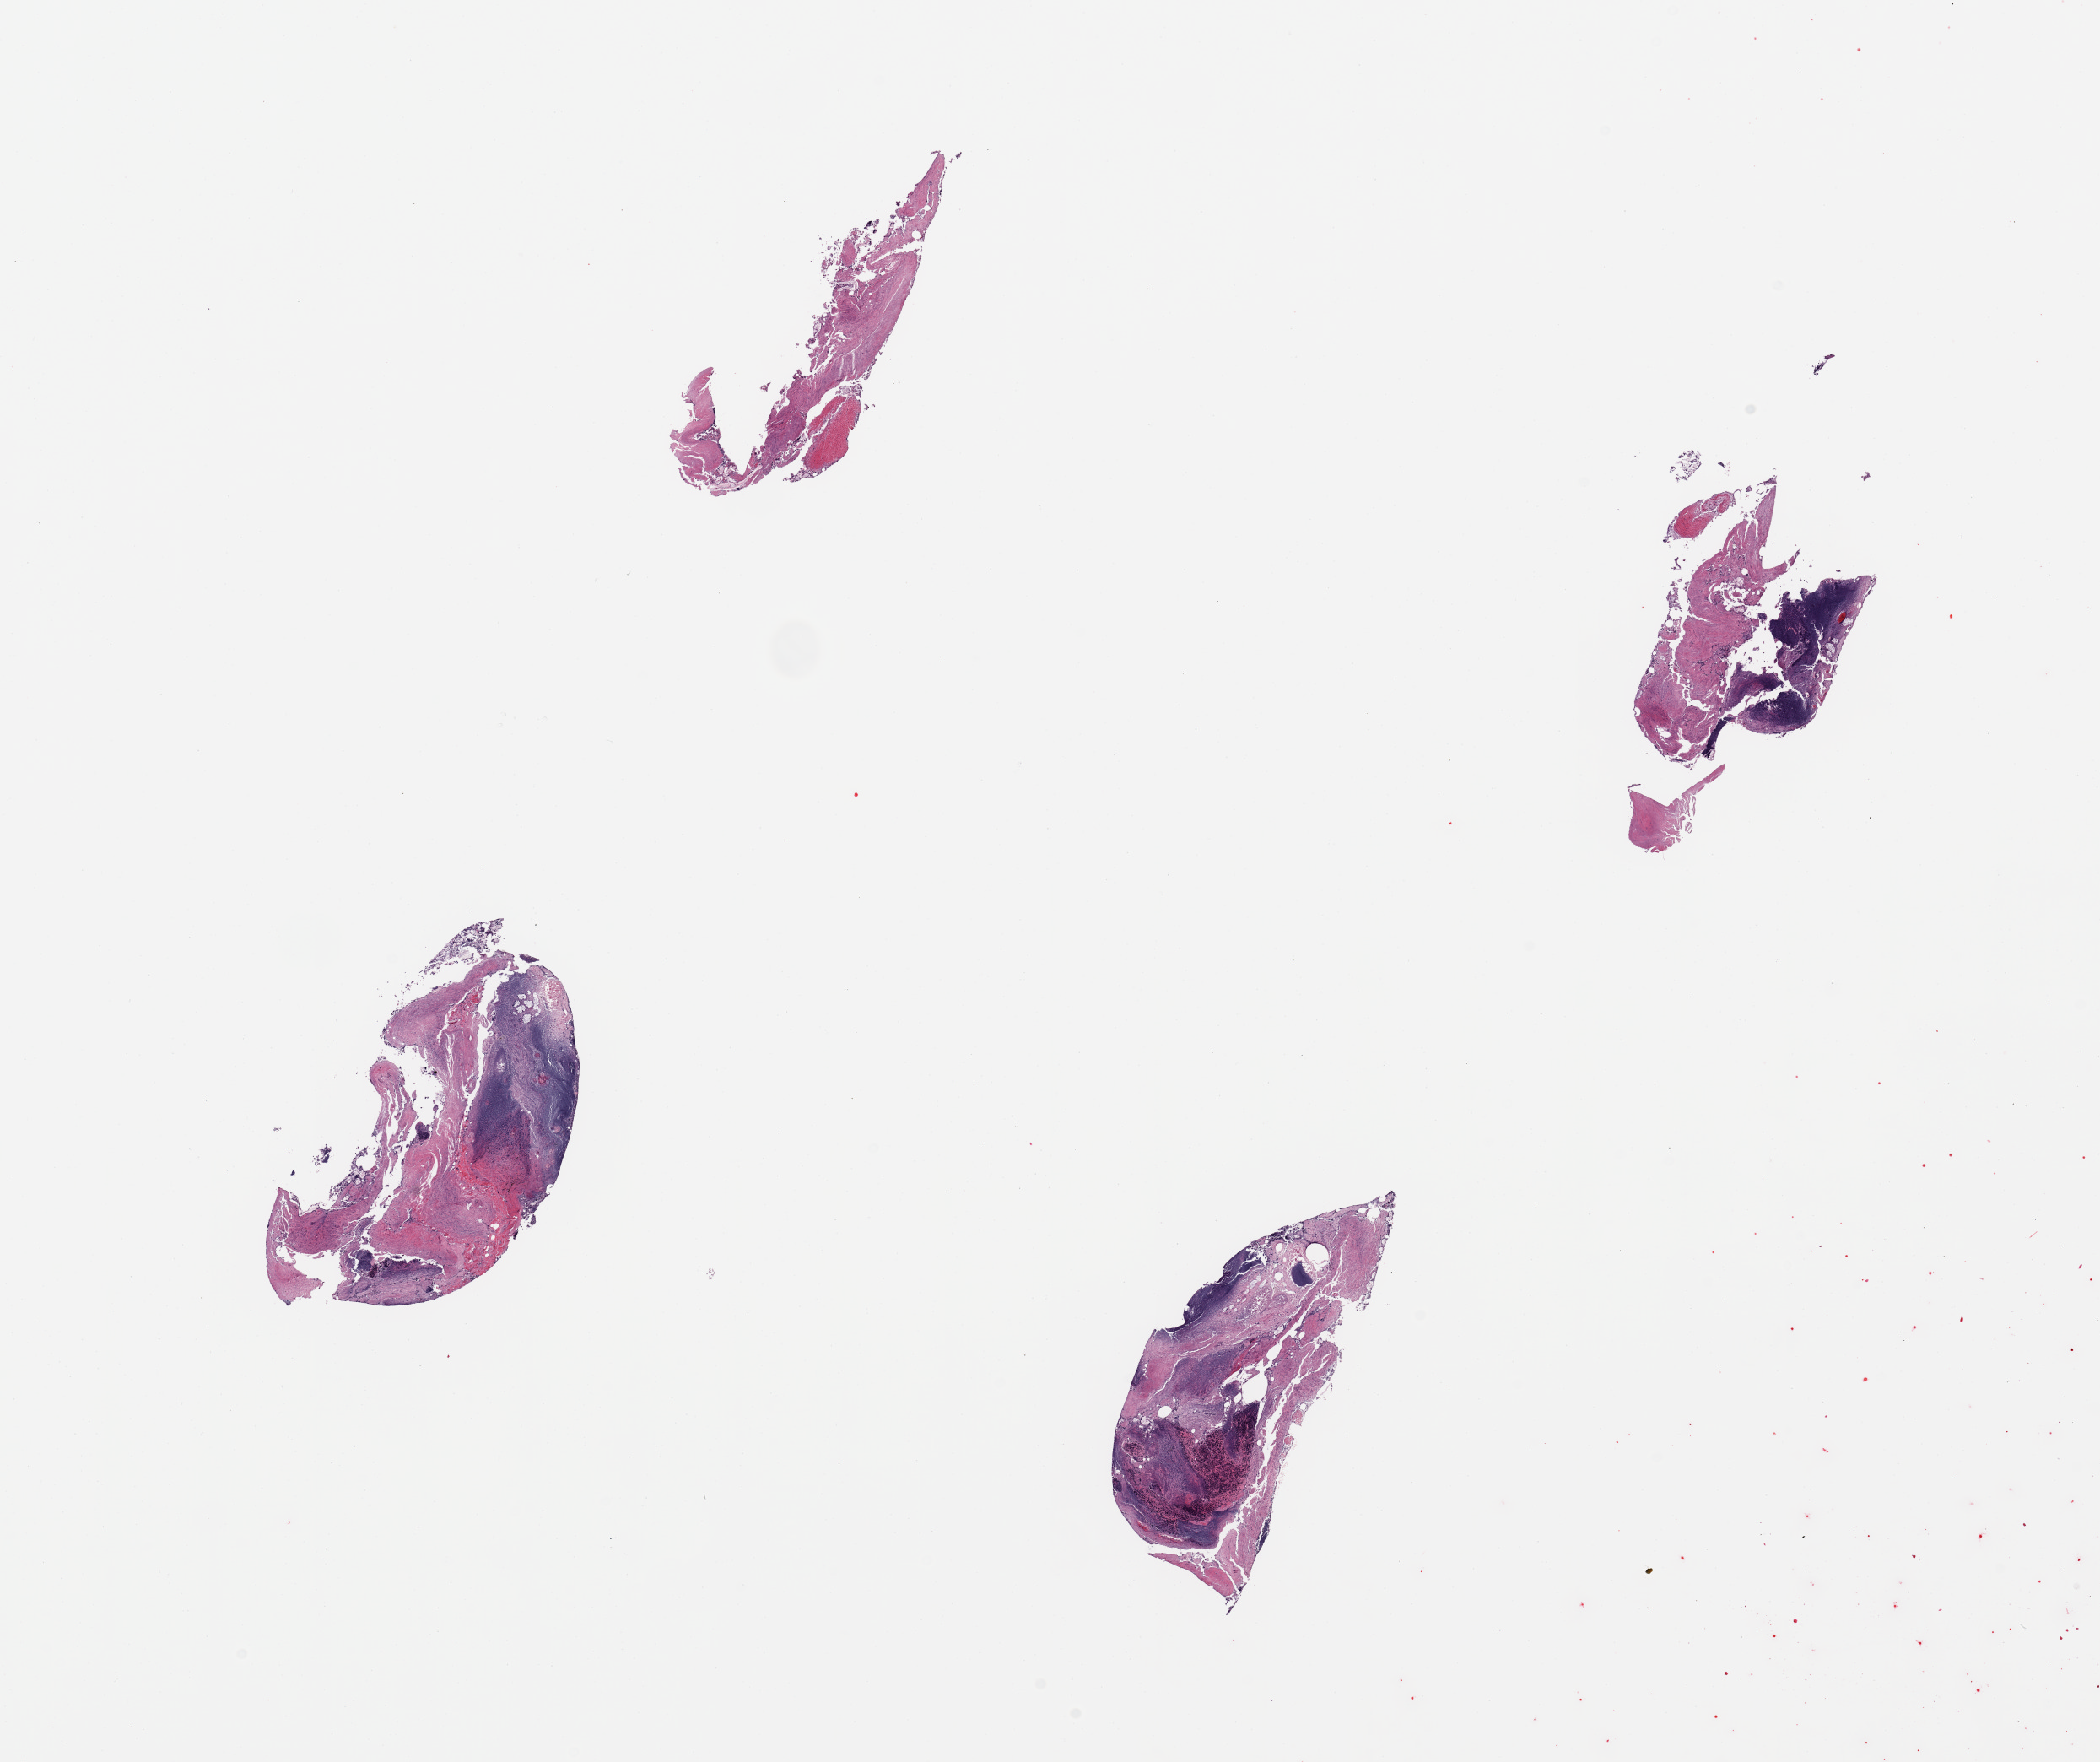
Digitized H&E-stained section, whole scanned area (about 19.7 x 16.5 mm) shown as a low-resolution overview. PAXgene-fixed, paraffin-embedded tissue. Section of ileum (target tissue). Tissue donor sample. Donor sex: male.
Reviewer comment on this tissue sample: 4 pieces; autolyzed mucosa and target lymphoid aggregates.